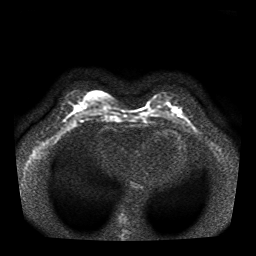
Breast MRI, one axial slice. Position 16 of 41 along the scan axis. Diffusion-weighted series; image 2 of 4 stored at this slice position (different b-values; order by instance number). 1.5 T. 5 mm slice thickness. 256 × 256 image matrix, field of view 330 × 330 mm. Female patient.
Annotated regions visible in this slice (manually delineated by an expert):
- tumour on diffusion-weighted imaging: bounding box [x1, y1, x2, y2] px = [176, 107, 182, 113]